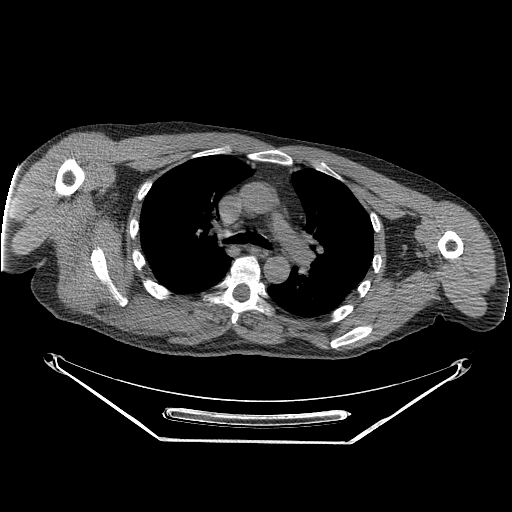
CT of an extremity soft-tissue mass (from a PET/CT study), one axial slice. Slice 182 of 267 in the series (ordered by position). 140 kVp. Soft-tissue window (W 400 / L 40 HU). 512 × 512 image matrix, field of view 500 × 500 mm. Male patient. Case-level facts recorded for this patient, not image findings: histological type: pleiomorphic spindle cell undifferentiated; grade: high; site of the primary tumour: right parascapusular.
Annotated regions visible in this slice (expert contour drawn on MRI and transferred to this co-registered scan by the dataset authors):
- gross tumour volume including surrounding oedema: bounding box [x1, y1, x2, y2] px = [89, 286, 216, 337]
- gross tumour volume (mass): [114, 290, 165, 328]